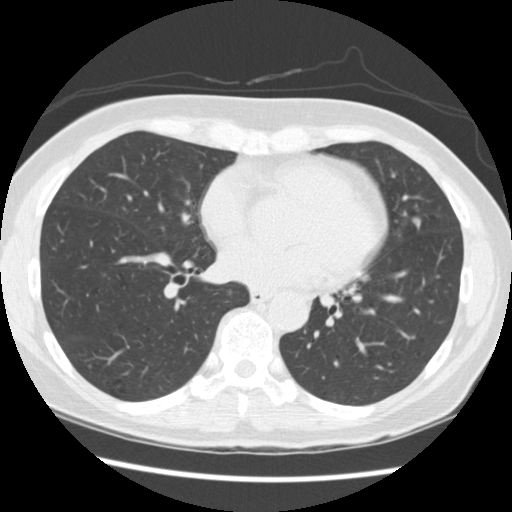
Axial slice from a low-dose chest CT screening exam; third annual screen; lung window (W 1500 / L -600 HU); 2.5 mm slice thickness; slice 143 of 262 in the series. Female, age 60 years at enrolment.
- Lesion marked by an expert reader, bounding box (x1, y1, x2, y2) in pixels: (394, 205, 437, 244).
- Screening reader's record for this exam (one nodule recorded; not confirmed to be the boxed lesion): non-calcified nodule or mass ≥4 mm, lingula, 6 × 5 mm, smooth margins, soft tissue attenuation, pre-existing on the prior screen: yes; interval growth: yes.
- Official screen result: positive, other.
- Participant outcome: lung cancer diagnosed 209 days after this screen — adenocarcinoma, NOS, lingula, poorly differentiated (G3), stage IA (AJCC 6th edition), 6 mm at pathology.